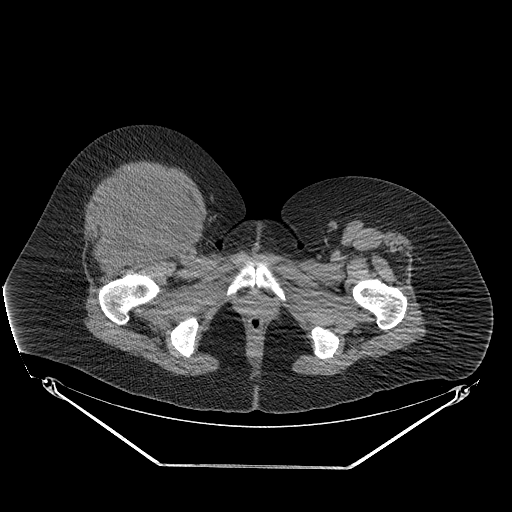
CT of an extremity soft-tissue mass (from a PET/CT study), one axial slice; reconstruction kernel STANDARD; 140 kVp; soft-tissue window (W 400 / L 40 HU); 3.75 mm slice thickness; 512 × 512 image matrix, field of view 500 × 500 mm. Female patient. Case-level facts recorded for this patient, not image findings: histological type: malignant solitary fibrous tumor; grade: intermediate; site of the primary tumour: right thigh.
Annotated regions visible in this slice (expert contour drawn on MRI and transferred to this co-registered scan by the dataset authors):
- gross tumour volume including surrounding oedema: bounding box (x1, y1, x2, y2) in pixels: (91, 171, 191, 241)
- gross tumour volume (mass): (91, 174, 188, 241)